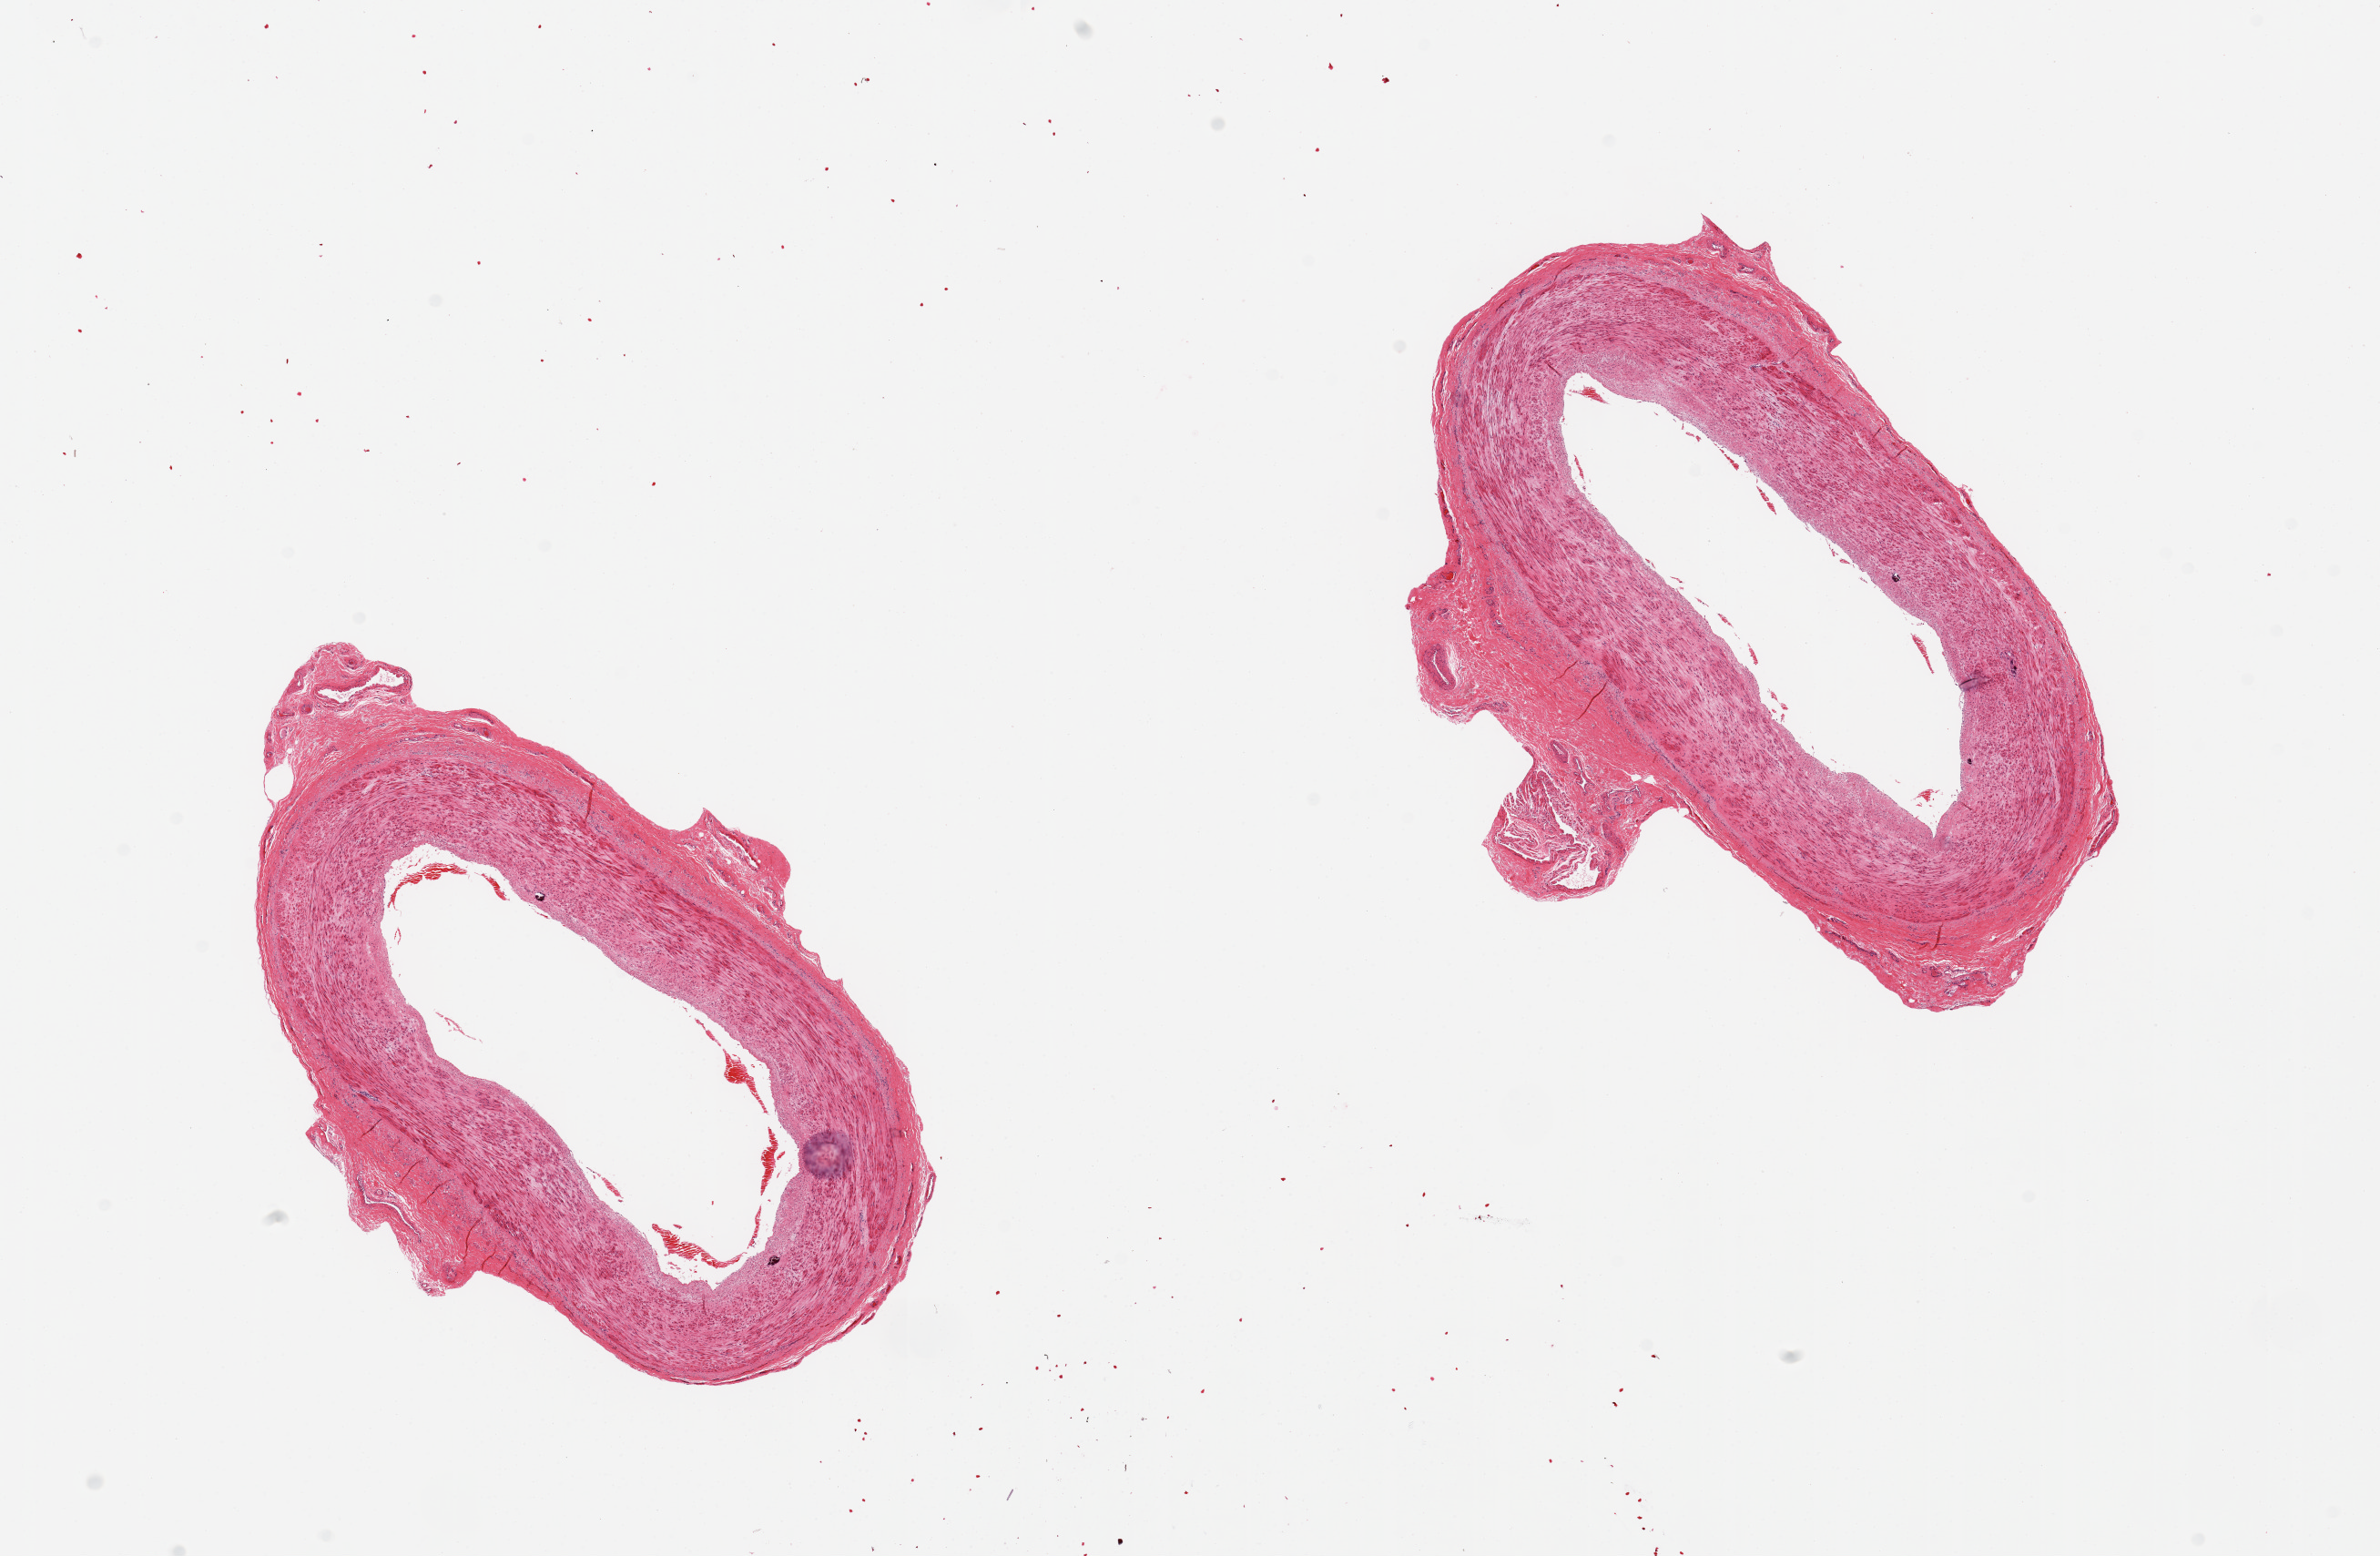
H&E whole-slide image — whole scanned area (about 20.7 x 13.5 mm) shown as a low-resolution overview; PAXgene-fixed paraffin-embedded (PFPE) section; sampled site (target tissue): tibial artery; donor tissue sample. Donor: male.
• reviewer comment on this tissue sample: 2 pieces; well trimmed; few very small foci of calcium